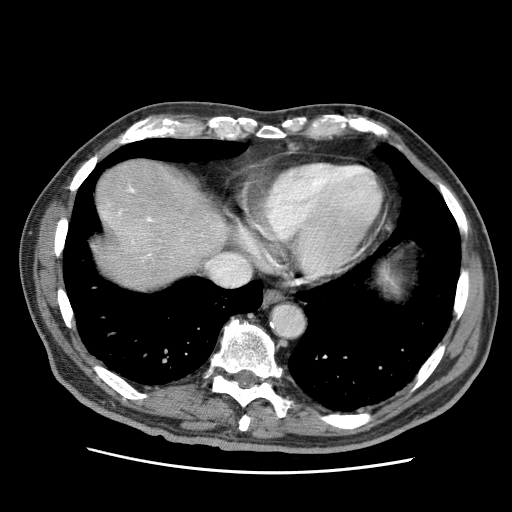
Contrast-enhanced abdominal CT (liver protocol), one axial slice. Slice 61 of 75 in the series (ordered by position). 120 kVp. Soft-tissue window (W 400 / L 40 HU). 2.5 mm slice thickness. 512 × 512 image matrix, field of view 360 × 360 mm. From the clinical record (not read from this slice): diagnosis: hepatocellular carcinoma (patient treated with transarterial chemoembolisation; whether this scan precedes or follows treatment is not stated here); TNM stage (as recorded): Stage-IIIA; Child-Pugh class: A; tumour nodularity: multinodular; tumour size: 13.9 cm.
Annotated regions visible in this slice (semi-automatic segmentation, software-assisted and operator-edited):
- liver parenchyma outside the tumour (the mass and vessels are separate outlines, so this box may not span the whole liver): bounding box (x1, y1, x2, y2) in pixels: (94, 159, 228, 290)
- liver vessels: (102, 186, 222, 258)